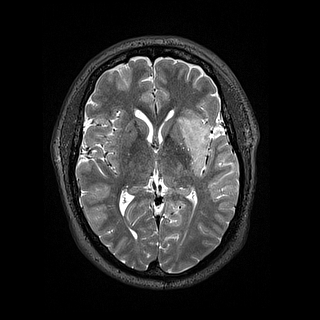
Brain MRI from a brain-tumour surgery series, one axial slice. Slice 84 of 144 in the series (ordered by position). 1.2 mm slice thickness. 320 × 320 image matrix. From the clinical record (not read from this slice): histopathology: Astrocytoma; WHO grade: 2; IDH mutation: yes.
Annotated regions visible in this slice (manually delineated by an expert):
- tumour: bounding box <178,110,211,176> (left, top, right, bottom; pixels)